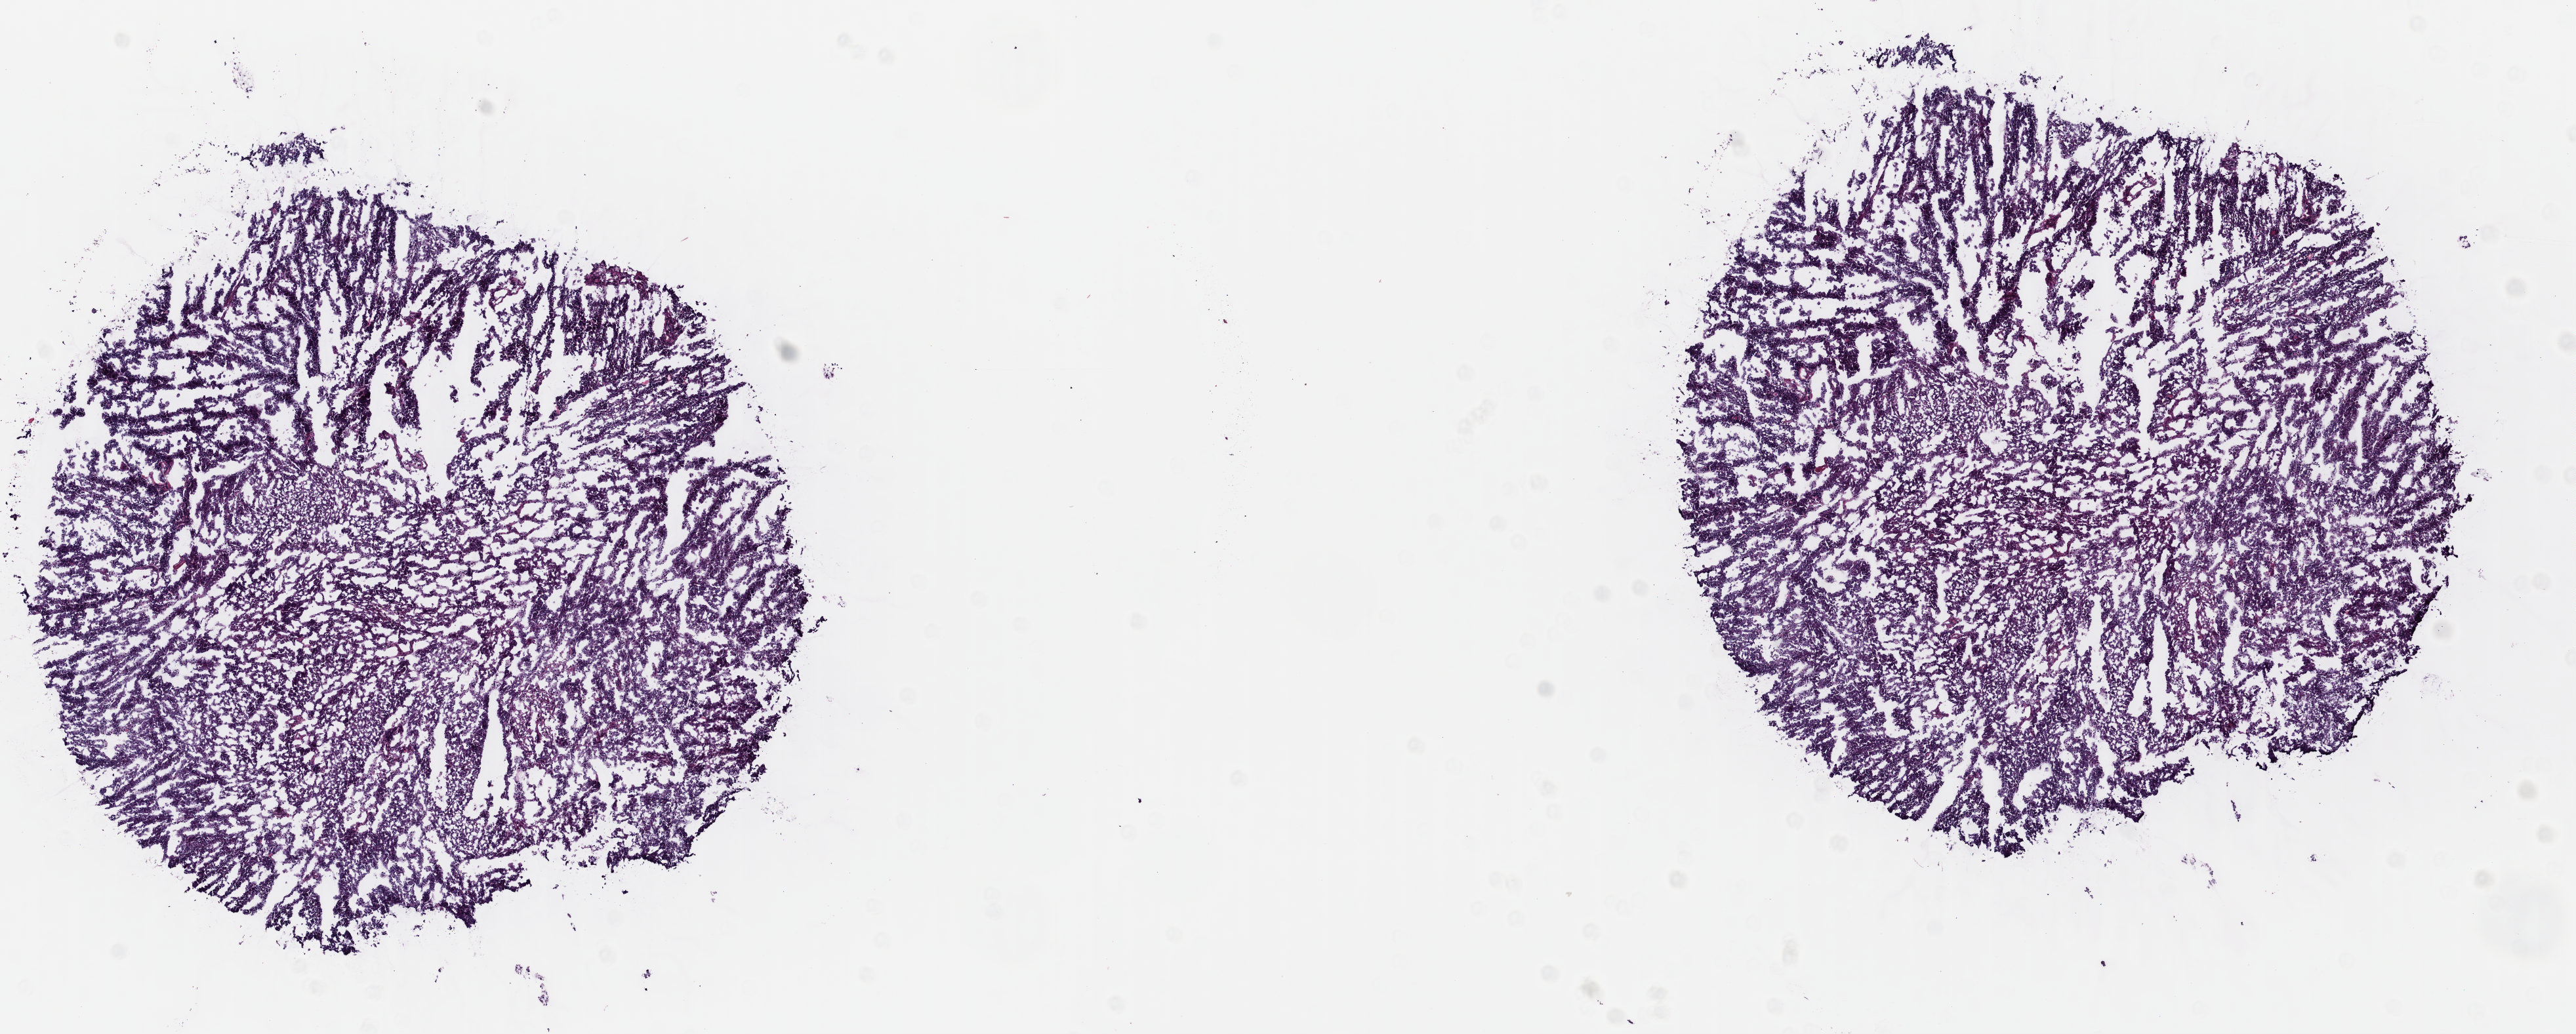
Hematoxylin and eosin (H&E) stained whole-slide image — shown as a low-resolution overview of the whole scanned area (about 15.4 x 6.2 mm, slide scanned at 40x). Frozen section. Uterus, primary tumour sample. Patient: female, age at initial diagnosis 65 years. Composition of this section per pathologist review: tumour cells 90%, tumour nuclei 90%.
Histologic diagnosis: Endometrioid adenocarcinoma, NOS (endometrium).